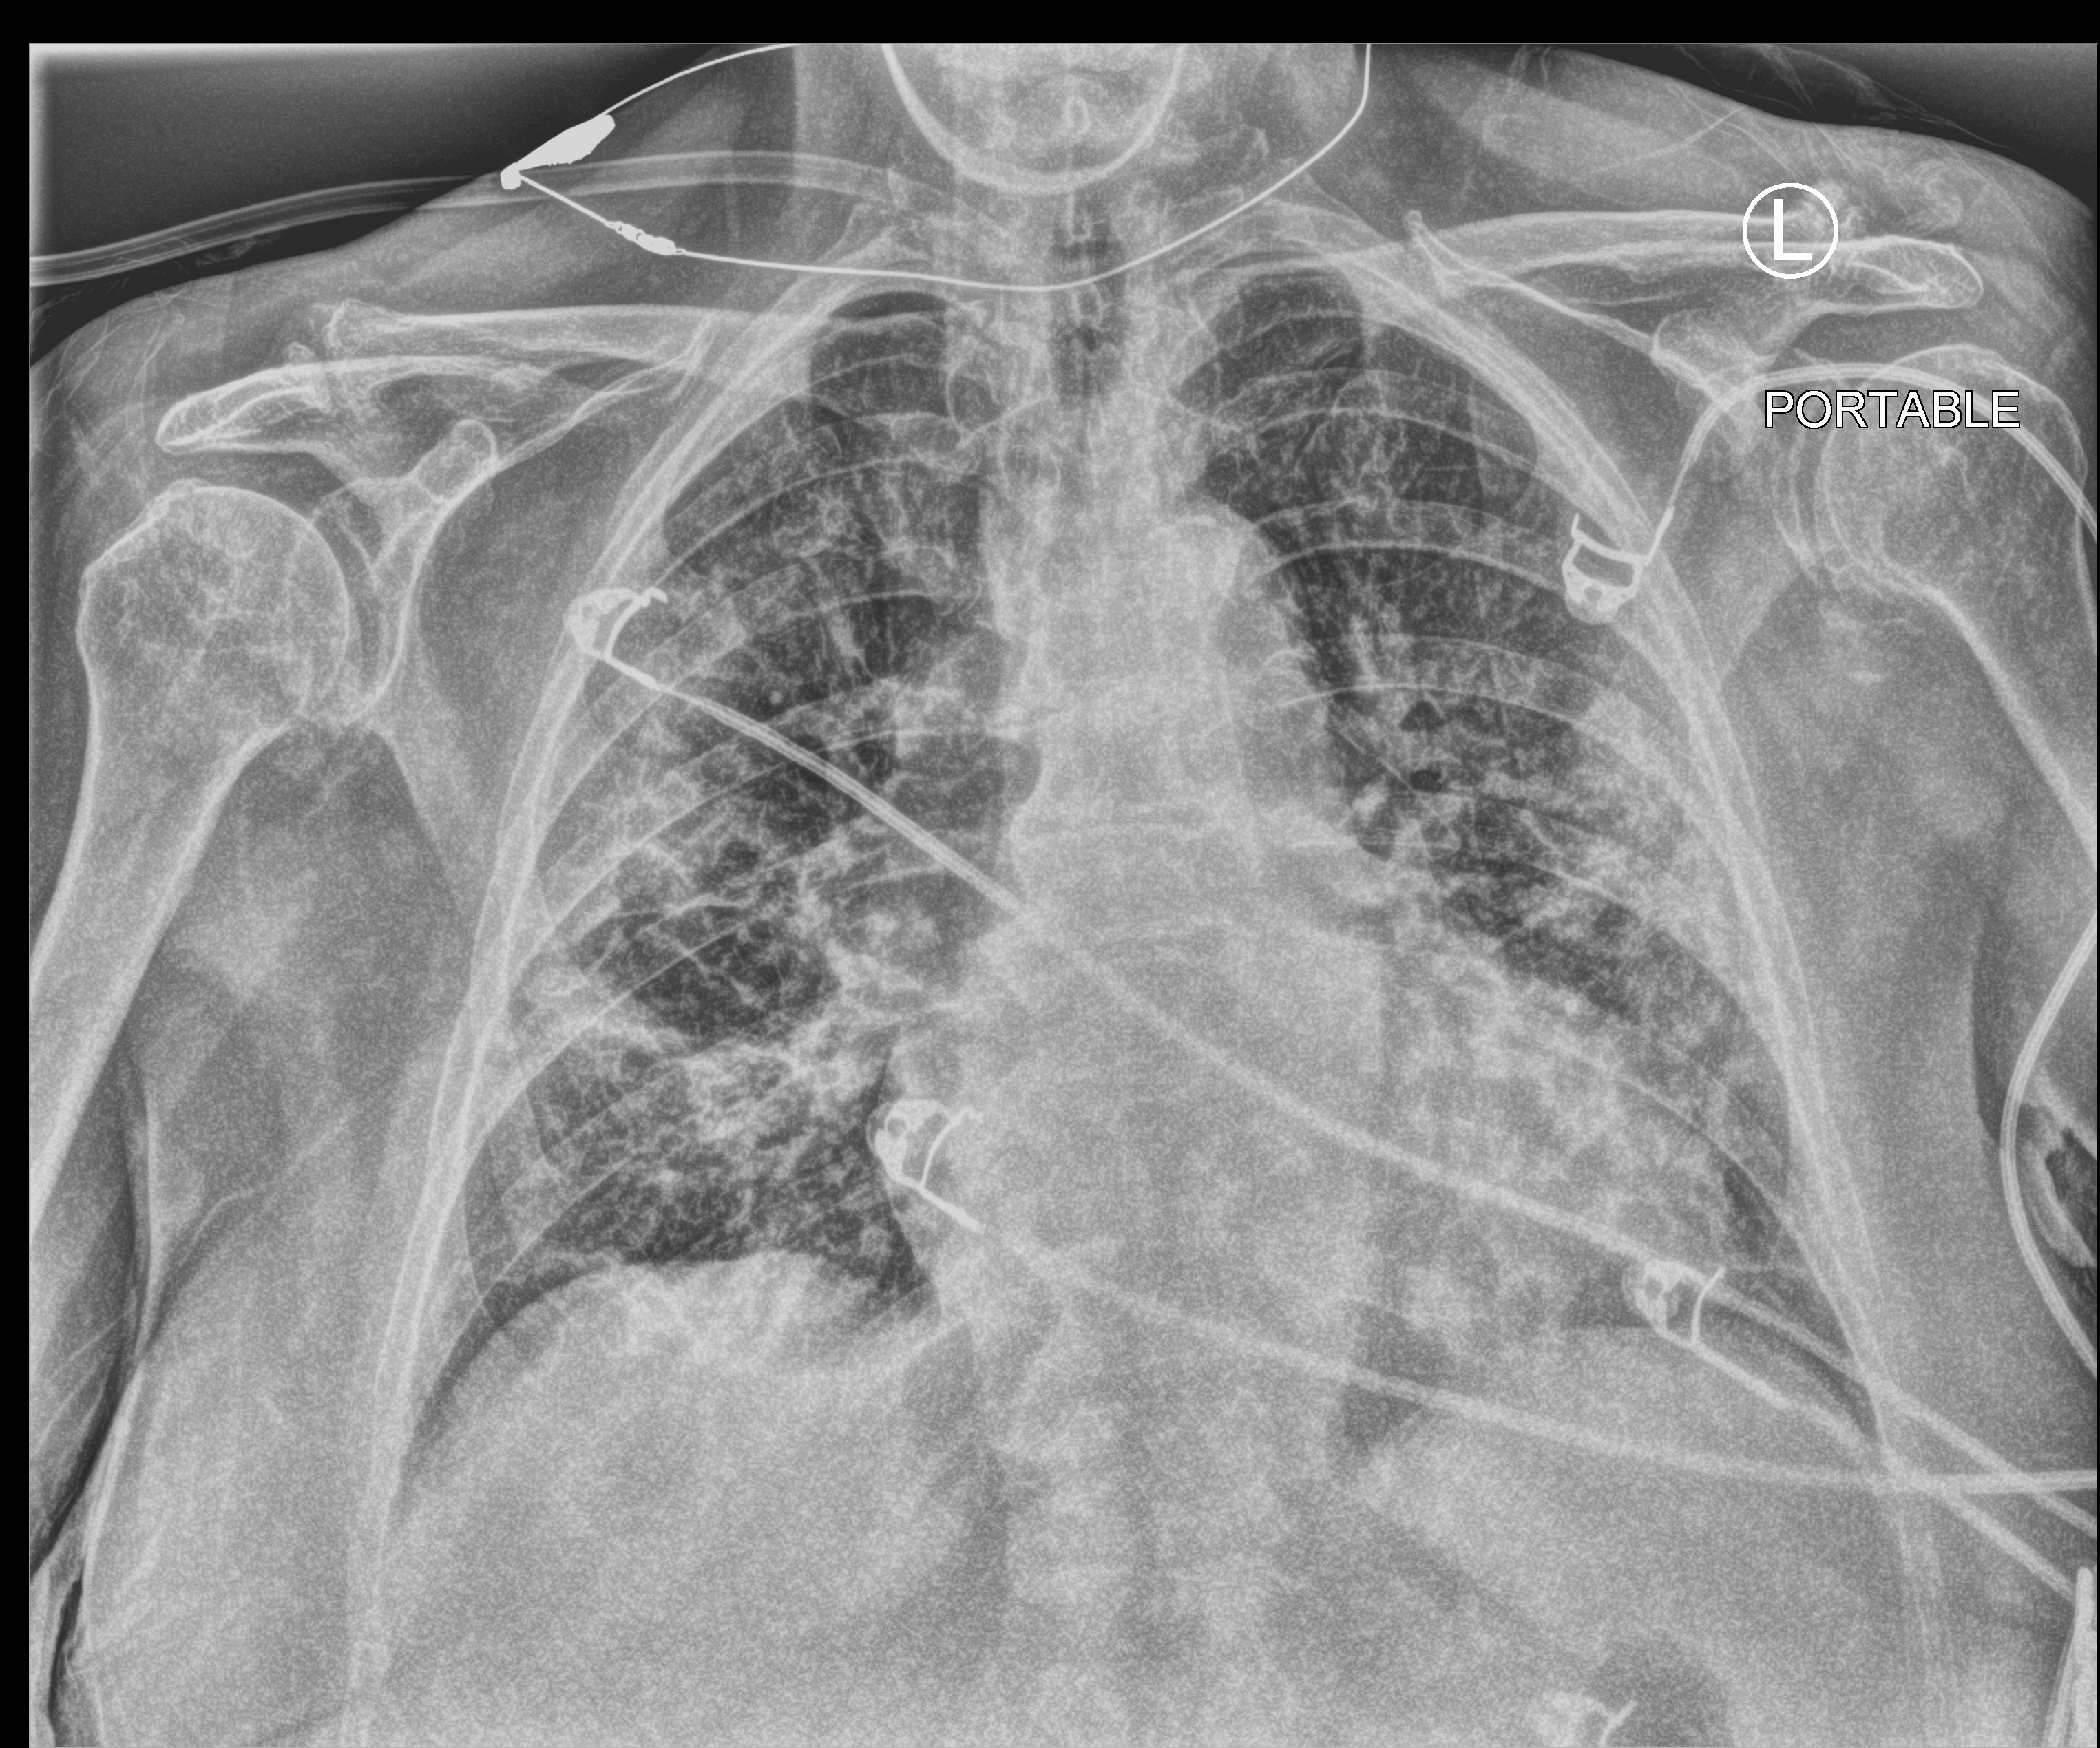
Portable chest radiograph. Female patient hospitalised with COVID-19, age 75–90 years.
Admission-level facts for this patient (not findings on this image; timing relative to this image not recorded):
- mechanically ventilated during this hospital stay: yes
- admitted to intensive care during this hospital stay: no